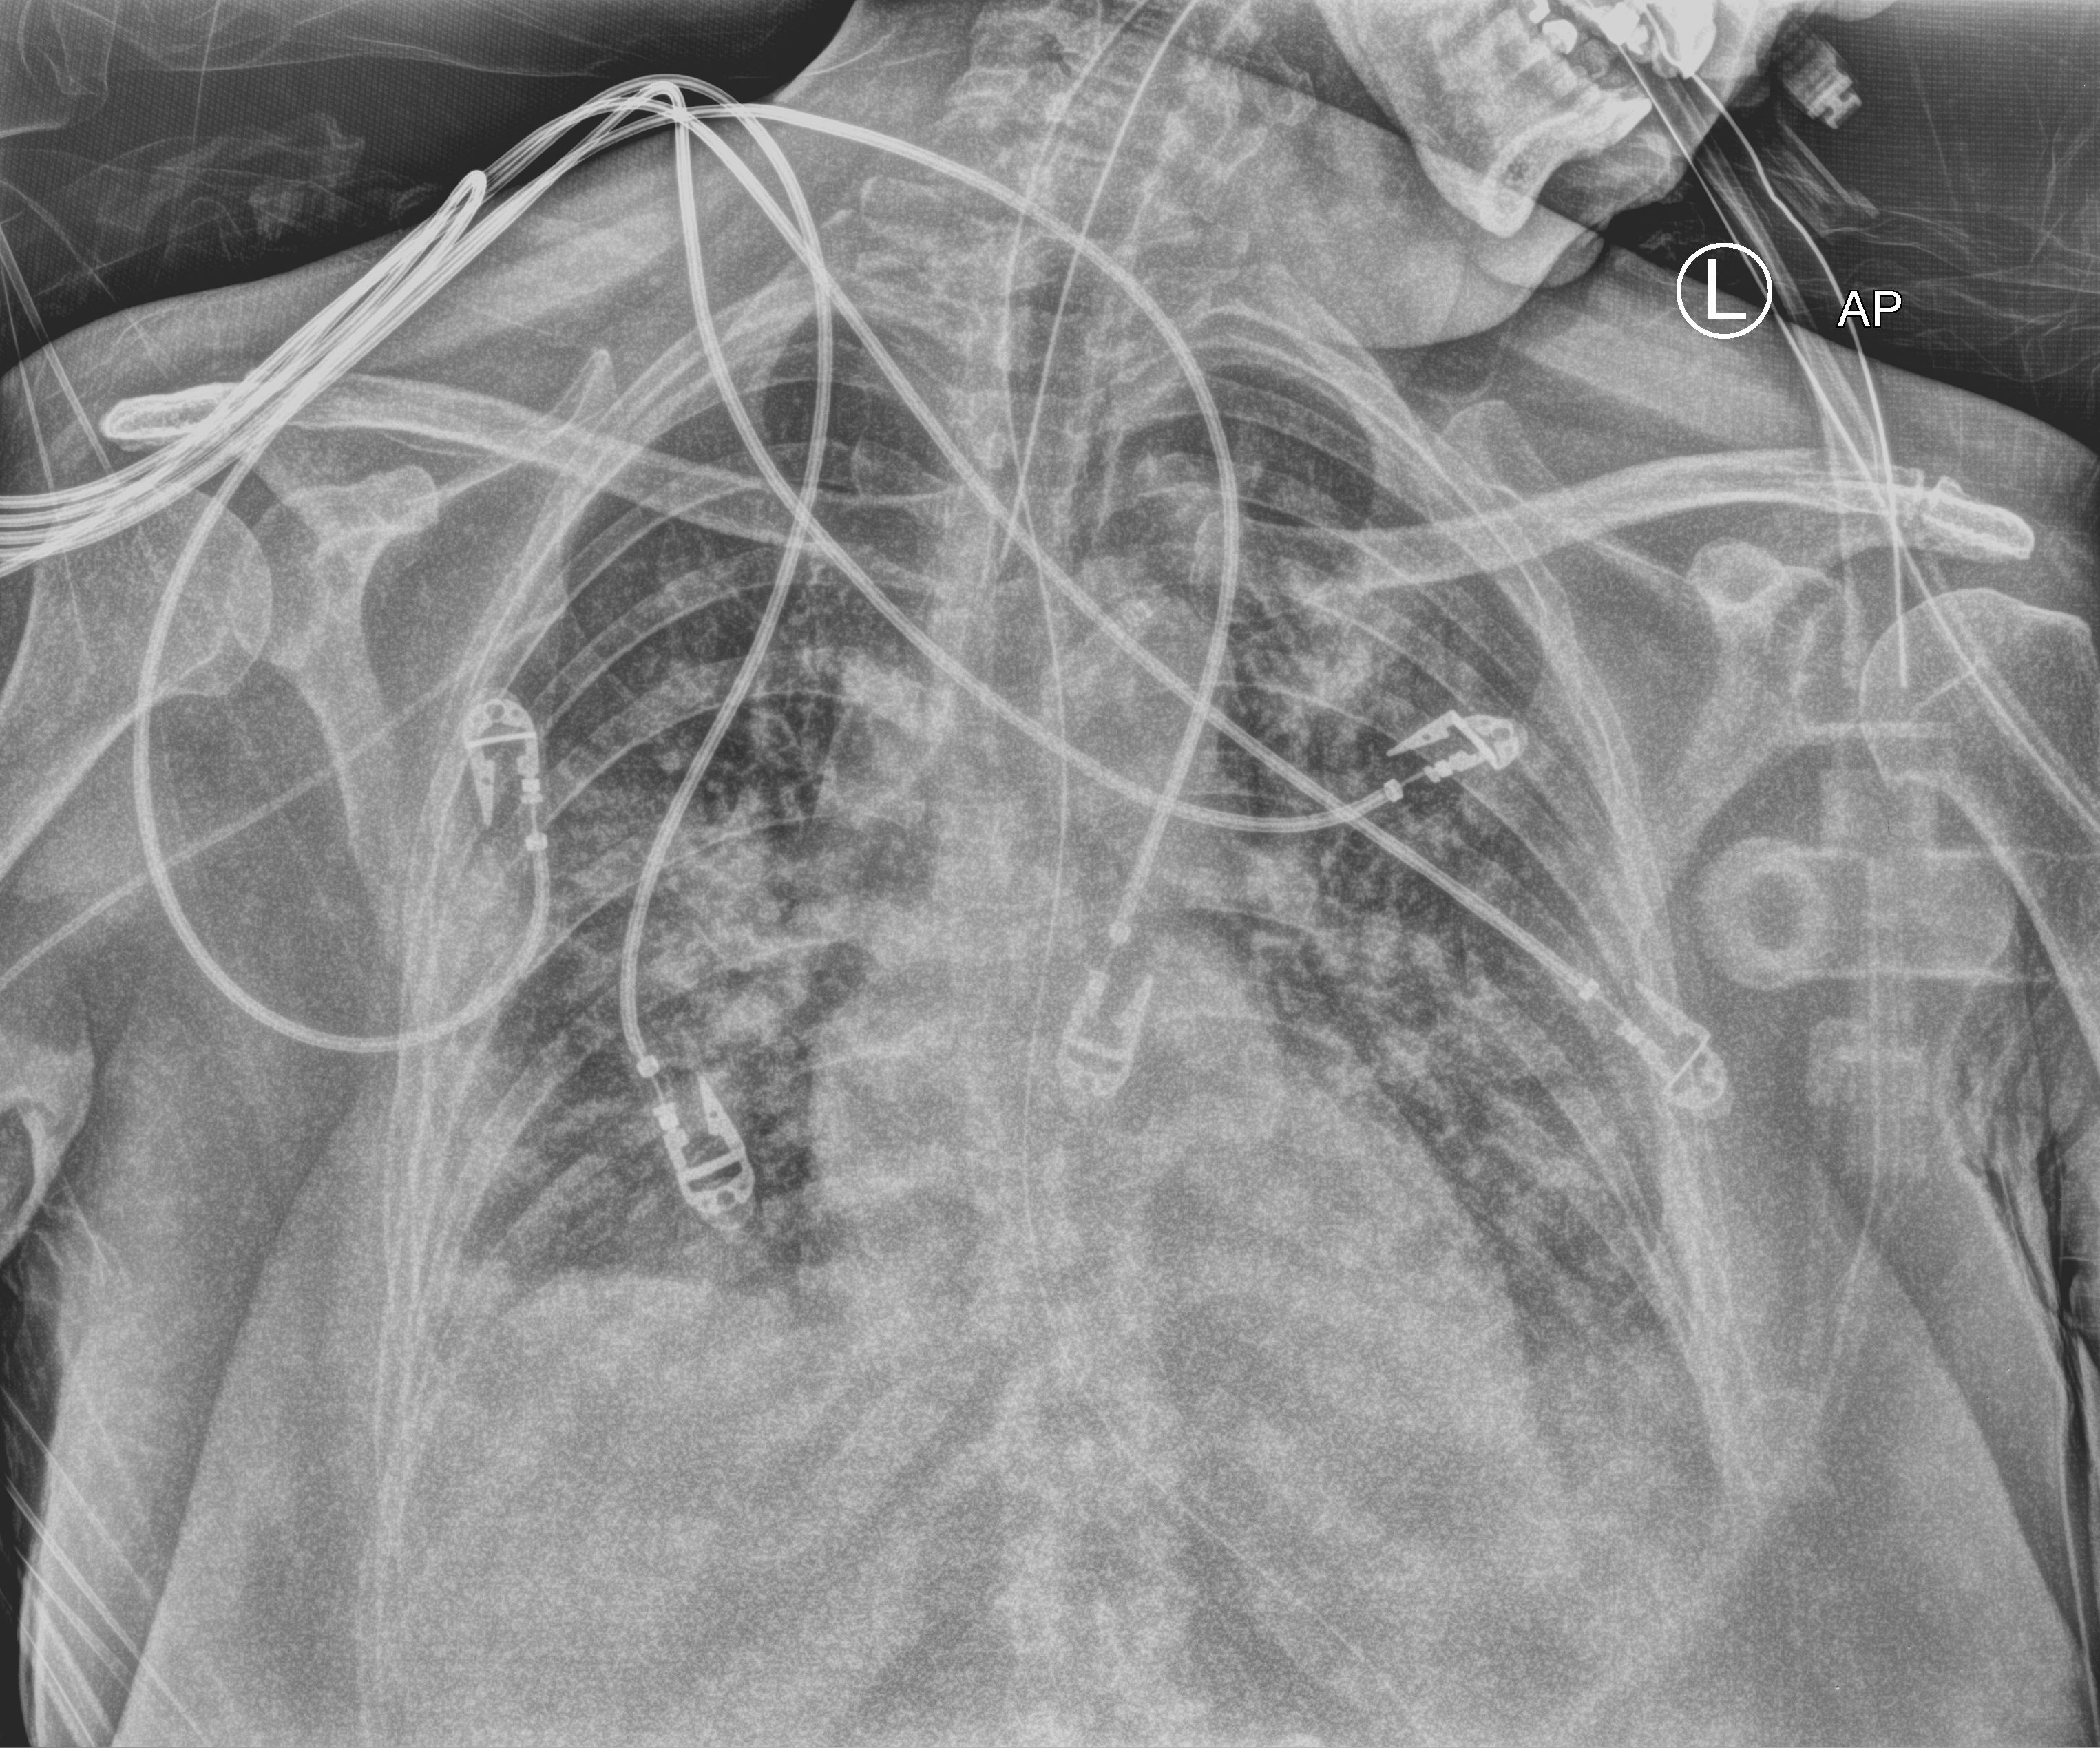
Bedside chest radiograph (computed radiography), anteroposterior (AP) projection. Patient hospitalised with COVID-19; female, aged 18–59 years.
Hospital-stay facts (about this admission, not read from this image; timing relative to this image not recorded): hypertension (admission record): no.